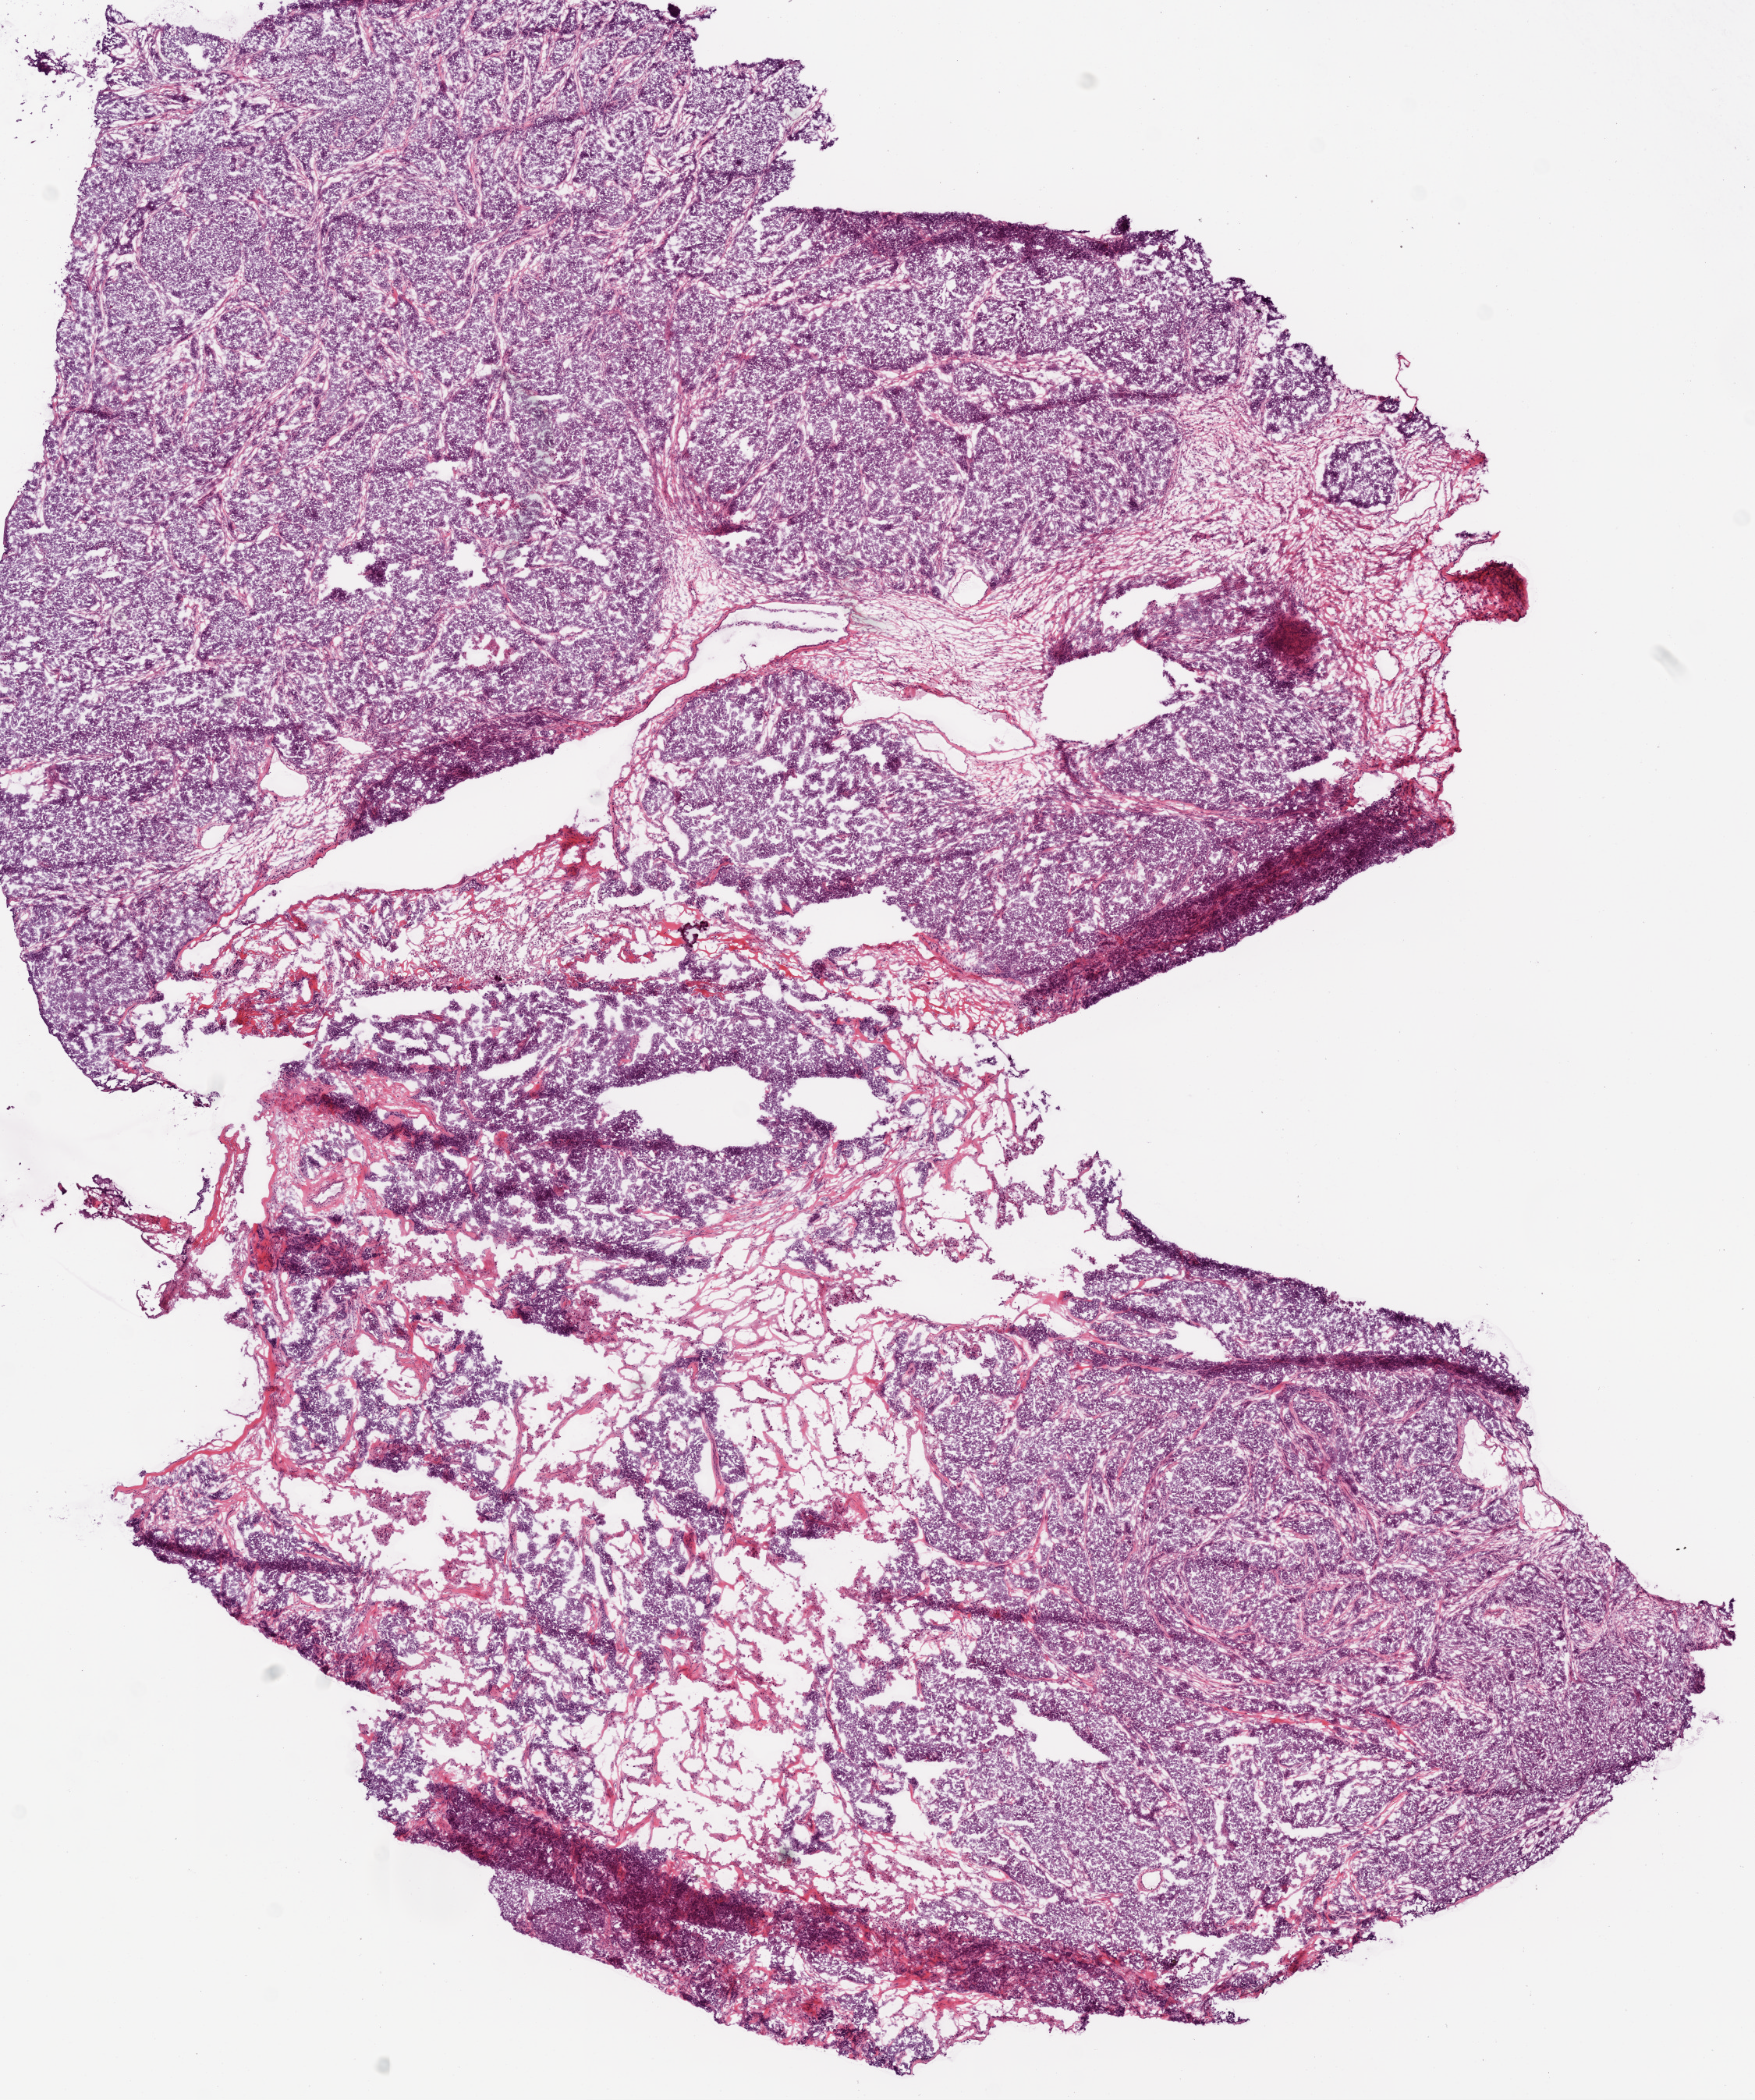
H&E whole-slide image, low-resolution overview of the scanned area, about 9.0 x 10.8 mm; frozen section from the bottom of the tissue portion; ovary, primary tumour sample. Female, age 57 years at initial diagnosis. Histologic grade: G3 (poorly differentiated). Composition of this section per pathologist review: tumour cells 78%, tumour nuclei 95%, normal cells 0%, stromal cells 20%, necrosis 2%.
Pathologic diagnosis: Serous cystadenocarcinoma, NOS. Laterality: bilateral. FIGO stage: IIIC.